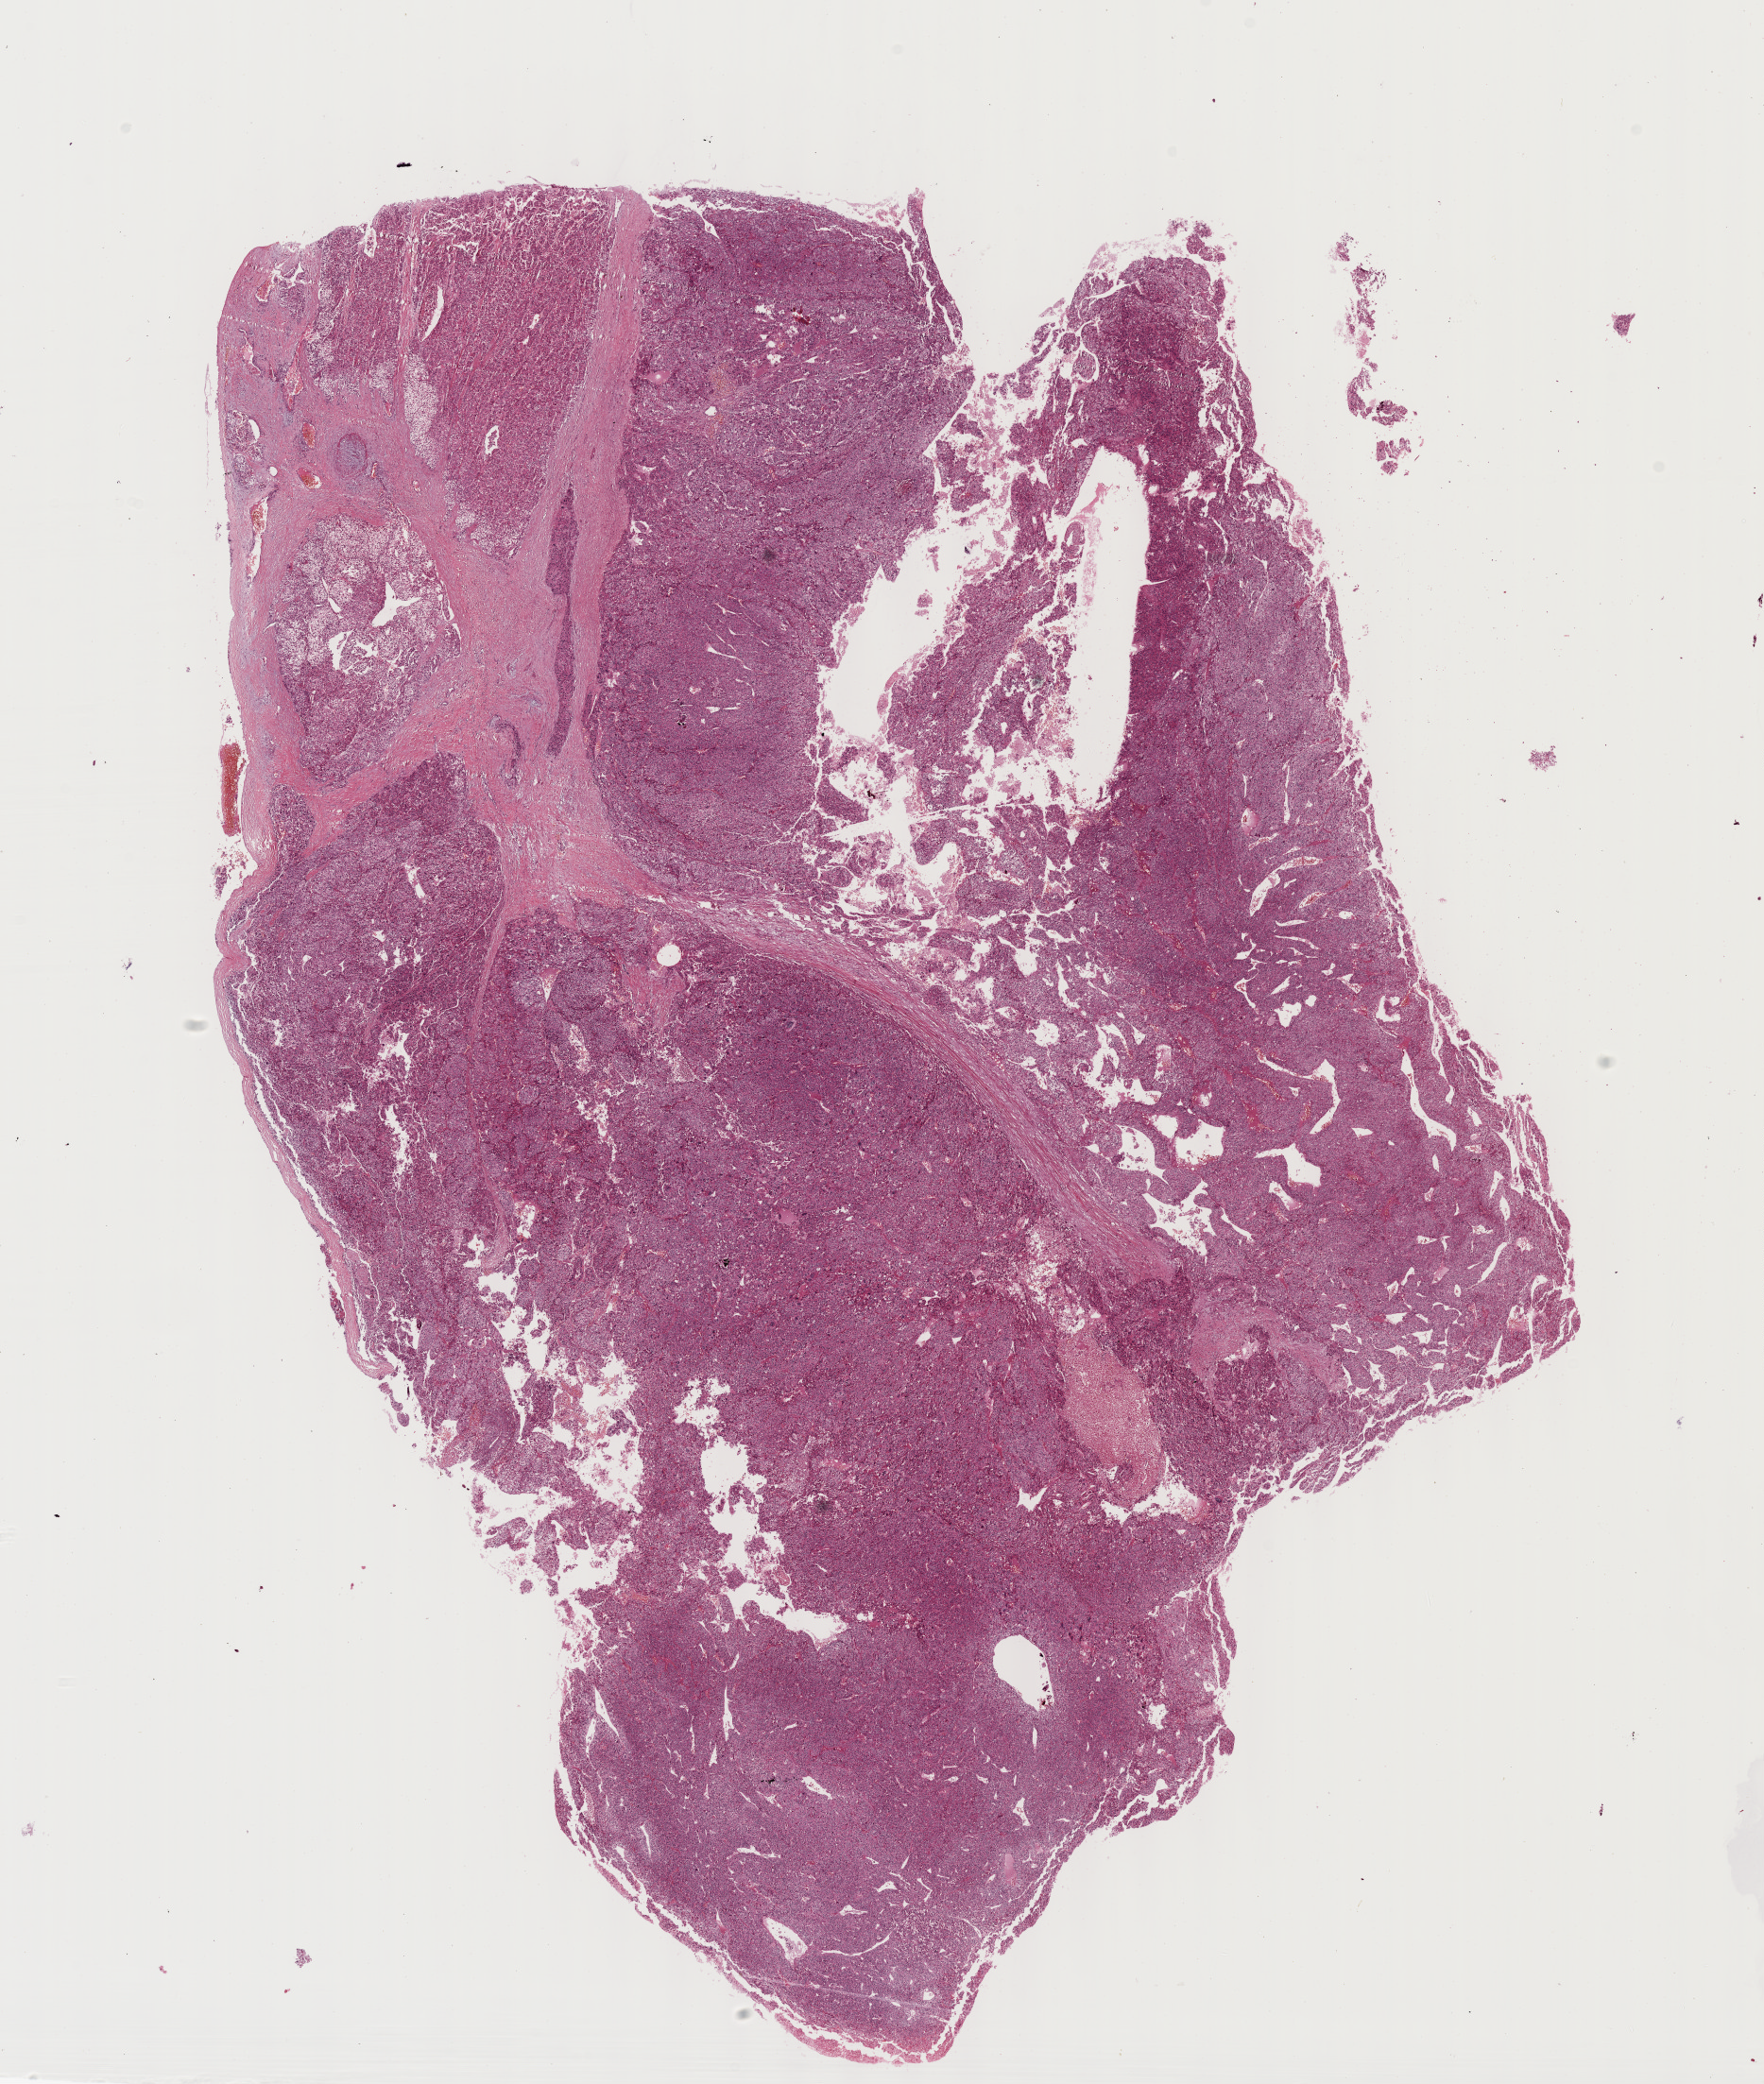
Whole-slide histology image, Hematoxylin and eosin (H&E) stained — a low-resolution overview of the entire scanned area, about 15.1 x 17.8 mm (slide scanned at 40x), formalin-fixed paraffin-embedded (FFPE) diagnostic section, sample: primary tumour, liver. Patient: female, age at initial diagnosis 39 years. Histologic grade: G3 (poorly differentiated).
AJCC pathologic stage: IIIA (6th edition). Diagnosis: Hepatocellular carcinoma, NOS.